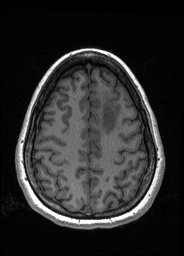
Pre-operative brain MRI before brain-tumour surgery, one axial slice; slice 56 of 176 in the series (ordered by position); T1-weighted post-contrast; 184 × 256 image matrix, field of view 180 × 250 mm. From the clinical record (not read from this slice): histopathology: Oligodendroglioma; WHO grade: 2; IDH mutation: yes; tumour location: Left Frontal.
Annotated regions visible in this slice (expert manual segmentation):
- tumour: bounding box <100,95,118,134> (left, top, right, bottom; pixels)